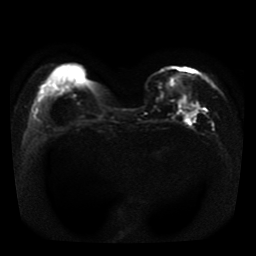
Breast MRI, one axial slice; position 11 of 41 along the scan axis; diffusion-weighted series; image 2 of 4 stored at this slice position (different b-values; order by instance number); 1.5 T; 5 mm slice thickness; 256 × 256 image matrix. Female patient.
Annotated regions visible in this slice (outlined manually by an expert reader):
- tumour on diffusion-weighted imaging: box from (x=179, y=98) to (x=199, y=118) px